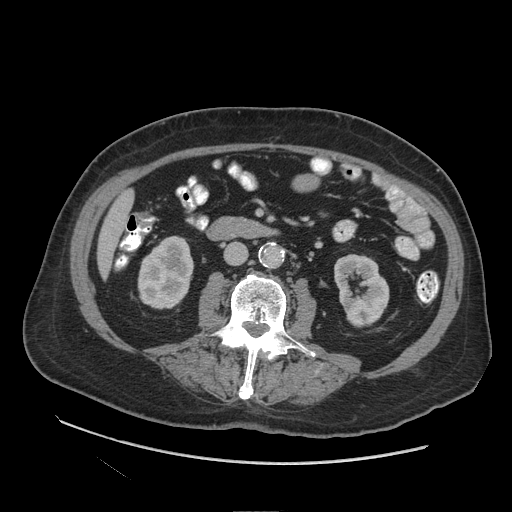
Contrast-enhanced abdominal CT (liver protocol), one axial slice. Slice 24 of 109 in the series (ordered by position). Reconstruction kernel STANDARD. 140 kVp. Soft-tissue window (W 400 / L 40 HU). 512 × 512 image matrix, field of view 420 × 420 mm. From the clinical record (not read from this slice): diagnosis: hepatocellular carcinoma (patient treated with transarterial chemoembolisation; whether this scan precedes or follows treatment is not stated here); TNM stage (as recorded): Stage-I; Child-Pugh class: A; tumour nodularity: uninodular.
Outlined on this slice (semi-automatic segmentation, software-assisted and operator-edited):
- liver parenchyma outside the tumour (the mass and vessels are separate outlines, so this box may not span the whole liver): box from (x=98, y=190) to (x=134, y=276) px